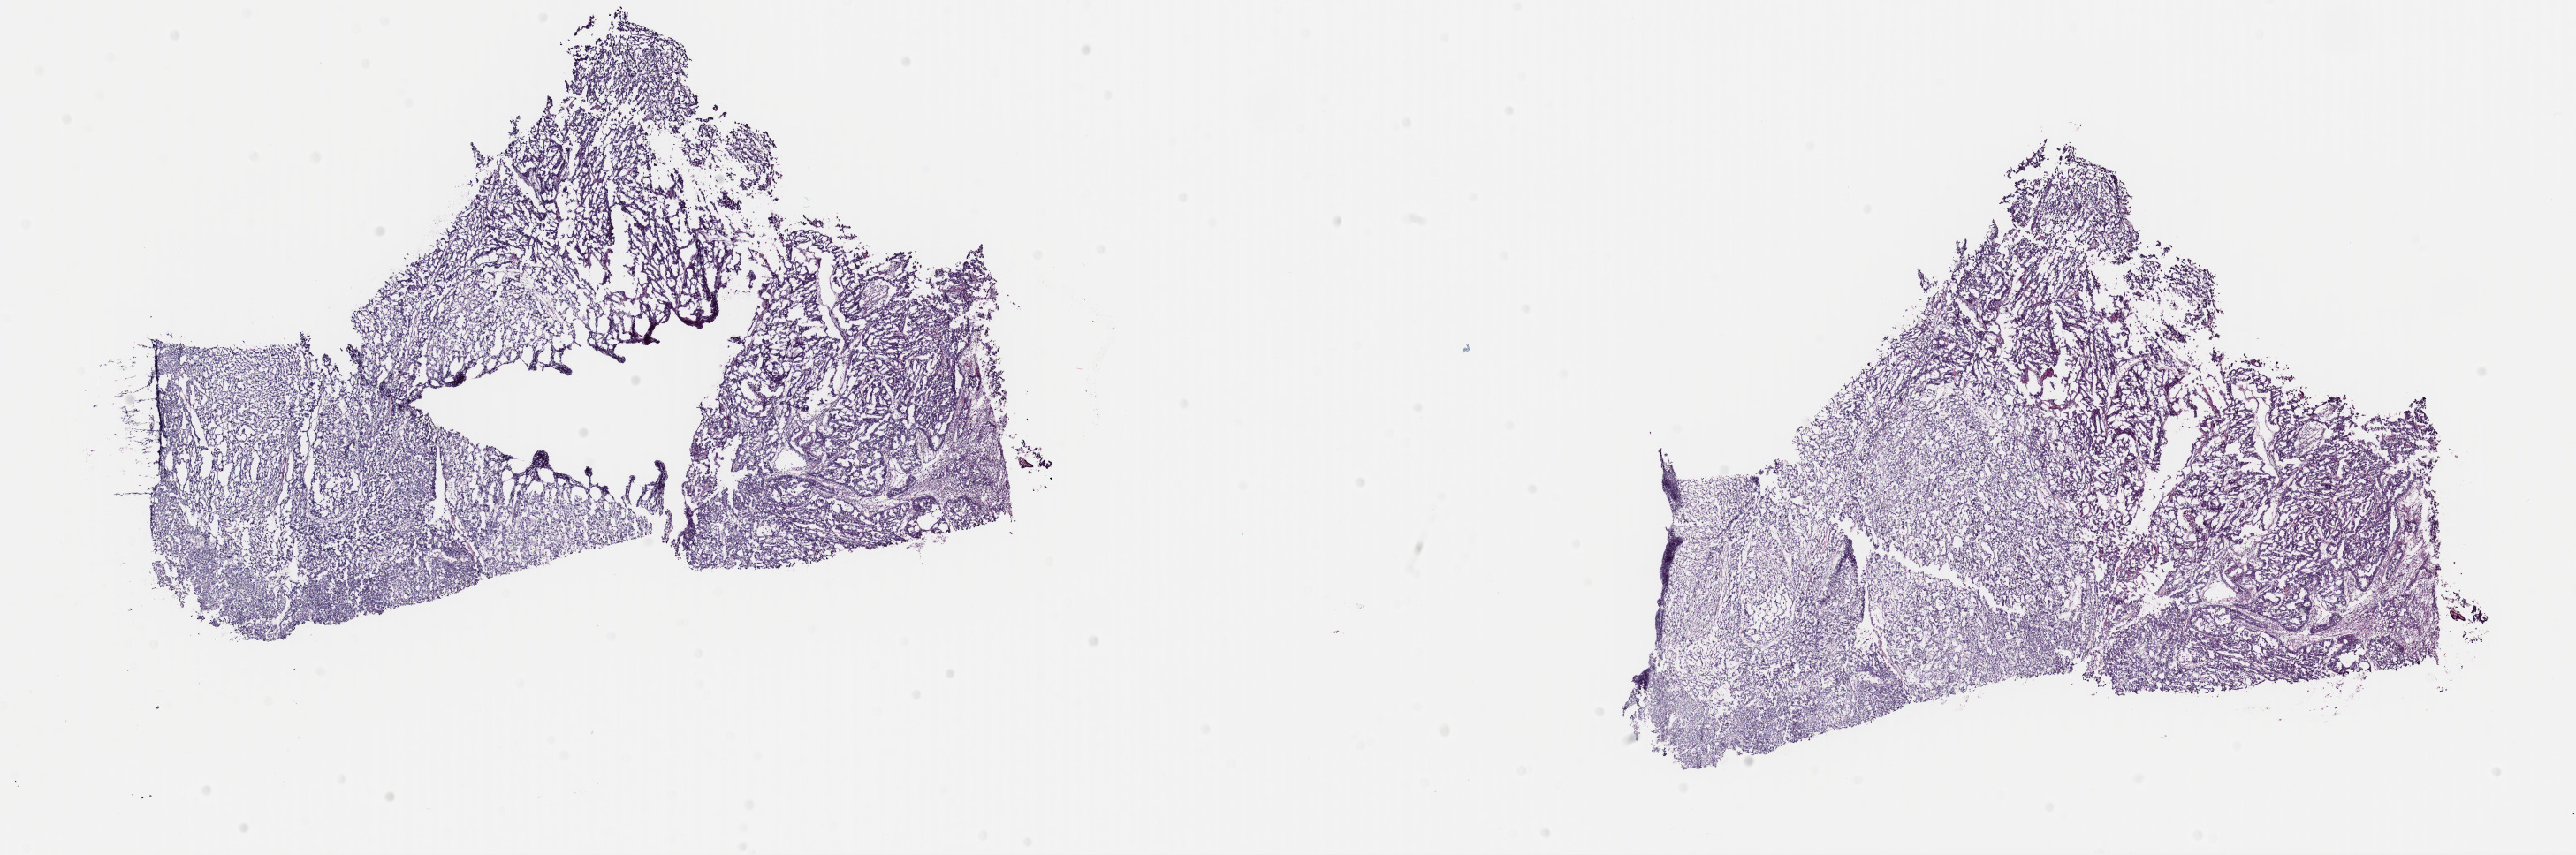
Digitized H&E-stained tissue section (whole slide) — whole scanned area (about 23.0 x 7.6 mm, acquisition: 40x scan) shown as a low-resolution overview; frozen section from the top of the tissue portion; primary tumour sample from the uterus. Female patient; age at initial diagnosis 56 years. Histologic grade: high grade. Composition of this section per pathologist review: tumour cells 100%, tumour nuclei 95%, normal cells 0%, stromal cells 0%, necrosis 0%. Inflammatory infiltration, as recorded: lymphocyte infiltration 1%, monocyte infiltration 0%, neutrophil infiltration 0%.
FIGO stage: IVB. Diagnosis: Serous cystadenocarcinoma, NOS (endometrium). Lymph nodes positive (case pathology): 12 of 29 examined.